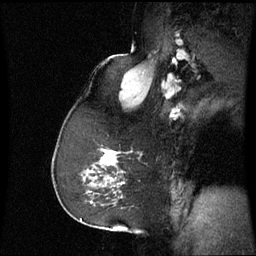
Breast MRI (dynamic contrast-enhanced), one sagittal slice; slice 41 of 60 in the series (ordered by position); dynamic contrast-enhanced series, image 2 of 3 at this slice position (ordered by acquisition); 1.5 T; TE 4.2 ms, TR 8.9 ms; 2.4 mm slice thickness; 256 × 256 image matrix. Patient: female, 59 years. From the clinical record (not read from this slice): setting: breast cancer imaged before/during neoadjuvant chemotherapy; receptor status: triple-negative.
Annotated regions visible in this slice (semi-automatically segmented with operator editing):
- analysis volume of interest (the breast-tissue region the enhancement analysis was run in; not a lesion): bounding box [x1, y1, x2, y2] px = [88, 148, 133, 197]
- tumour enhancement mask (voxels above the 70 % enhancement threshold inside the analysis volume of interest): [102, 152, 117, 165]